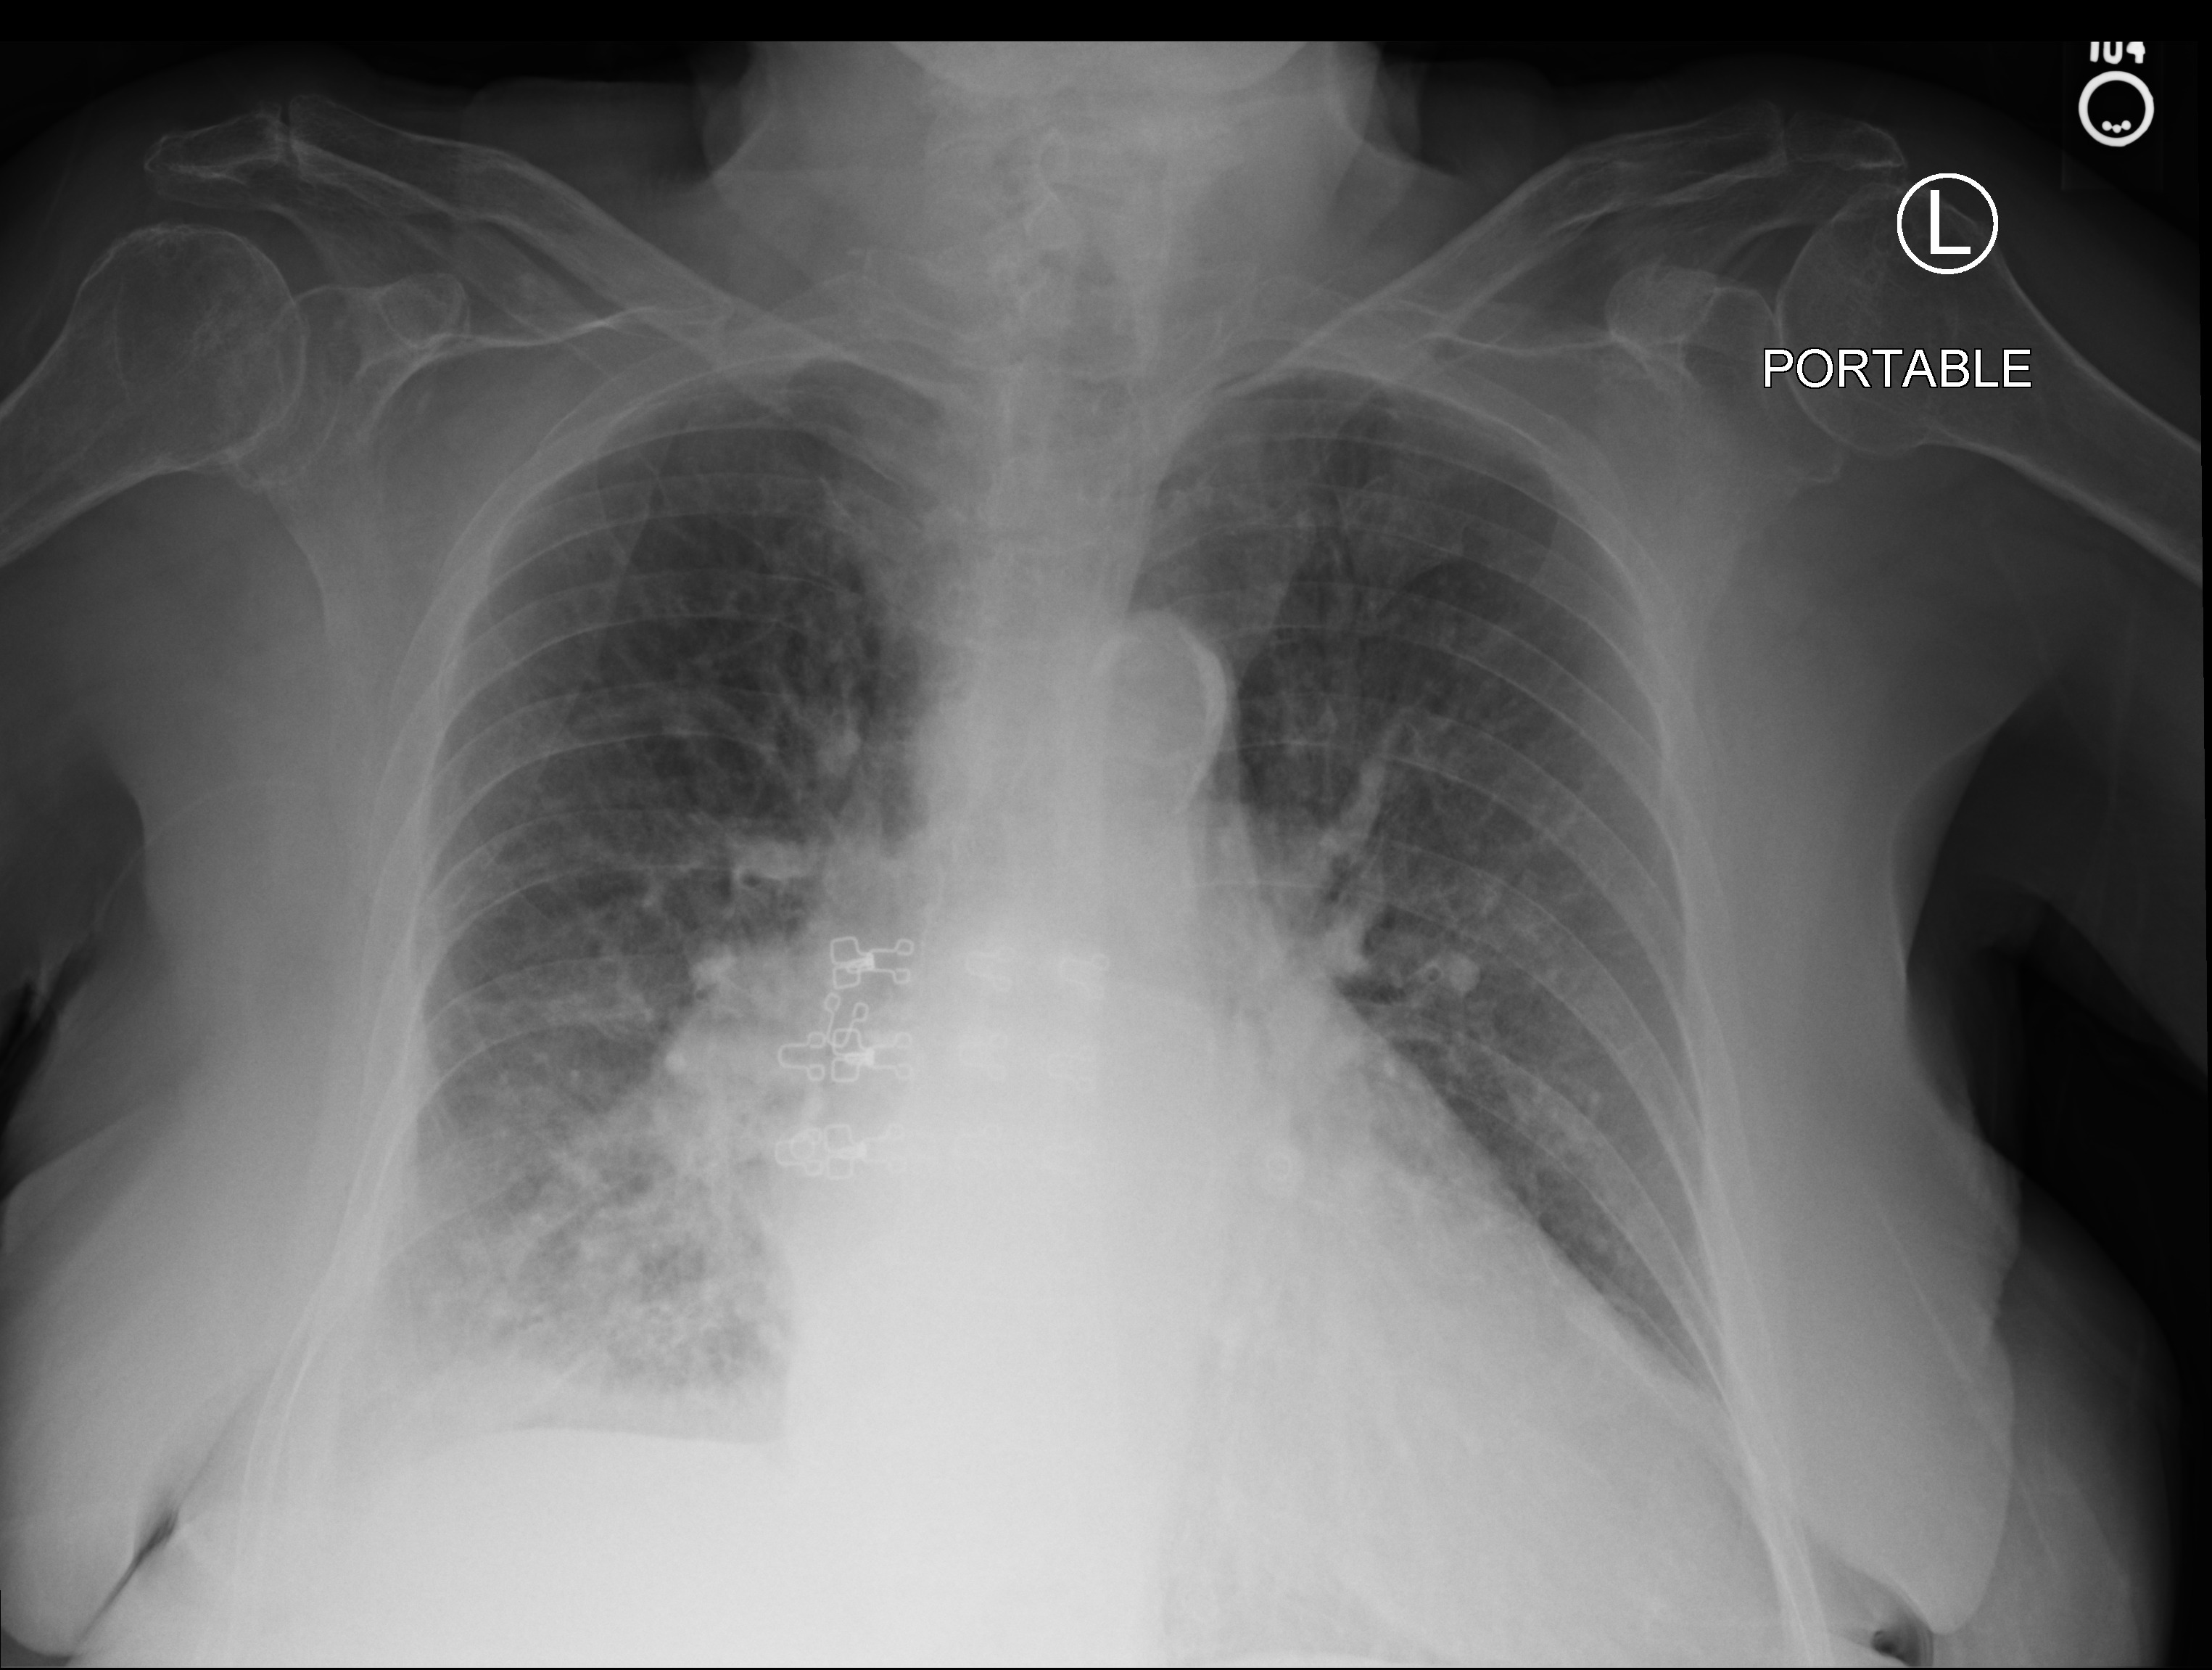
Chest X-ray (portable); anteroposterior (AP) projection. Female patient hospitalised with COVID-19, age 75–90 years.
Admission-level facts for this patient (not findings on this image; timing relative to this image not recorded): chronic kidney disease (admission record): no; admitted to intensive care during this hospital stay: yes.